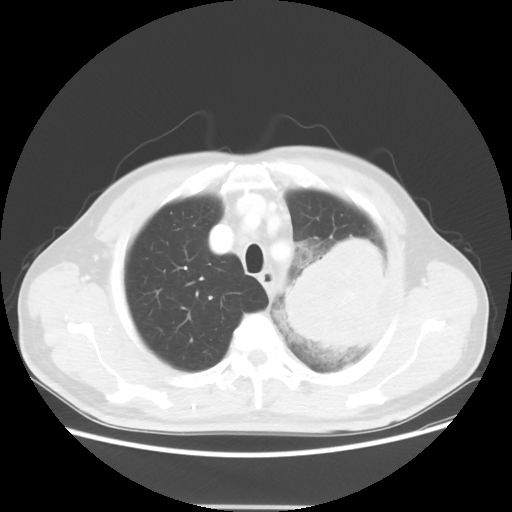
Chest CT, one axial slice. Position 45 of 53 along the scan axis. 100 kVp. Lung window (W 1500 / L -600 HU). 512 × 512 image matrix. Patient: male, 60 years. Case-level facts recorded for this patient, not image findings: clinical TNM (as recorded): T4 N1 M1a; histopathological grade: G3.
Annotated regions visible in this slice (bounding box drawn by a radiologist):
- lung tumour (recorded histology: large cell carcinoma): bounding box [x1, y1, x2, y2] px = [260, 212, 390, 370]